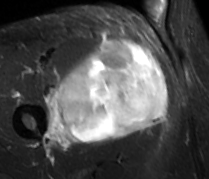
MRI of an extremity soft-tissue mass, one axial slice. Slice 46 of 89 in the series (ordered by position). STIR. MR volume resampled by the dataset authors to the PET/CT grid (not the native acquisition matrix). 3.27 mm slice thickness. 209 × 179 image matrix, field of view 204 × 175 mm. Male patient. Case-level facts recorded for this patient, not image findings: histological type: undifferentiated - pleiomorphic; grade: high; site of the primary tumour: right thigh.
Structures marked on this image (expert contour drawn on MRI and transferred to this co-registered scan by the dataset authors):
- gross tumour volume including surrounding oedema: bounding box (x1, y1, x2, y2) in pixels: (43, 39, 168, 147)
- gross tumour volume (mass): (55, 39, 168, 143)